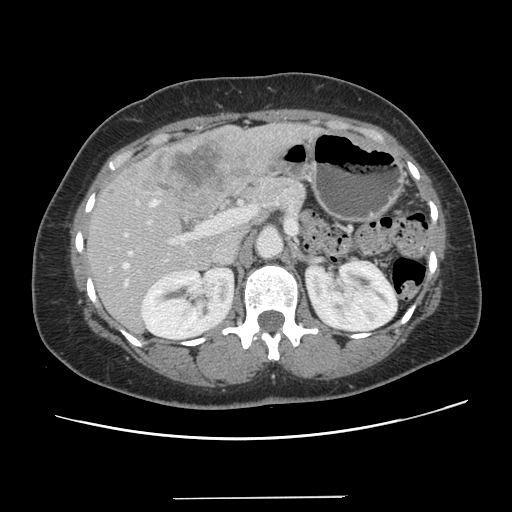
Contrast-enhanced abdominal CT, one axial slice; slice 70 of 141 in the series (ordered by position); 120 kVp; soft-tissue window (W 400 / L 40 HU); 2.5 mm slice thickness; 512 × 512 image matrix. Female patient, age 53 years. From the clinical record (not read from this slice): diagnosis: colorectal cancer liver metastases, imaged before liver resection; multiple liver metastases: no; largest metastasis: 14.5 cm; disease in both lobes: yes.
Structures marked on this image (outlined manually by an expert reader):
- hepatic veins: bounding box (x1, y1, x2, y2) in pixels: (123, 251, 131, 285)
- liver: (89, 124, 312, 331)
- planned liver remnant (the part of the liver to remain after resection): (89, 208, 249, 331)
- portal vein (with intrahepatic branches): (124, 199, 251, 244)
- liver metastasis: (138, 139, 250, 199)